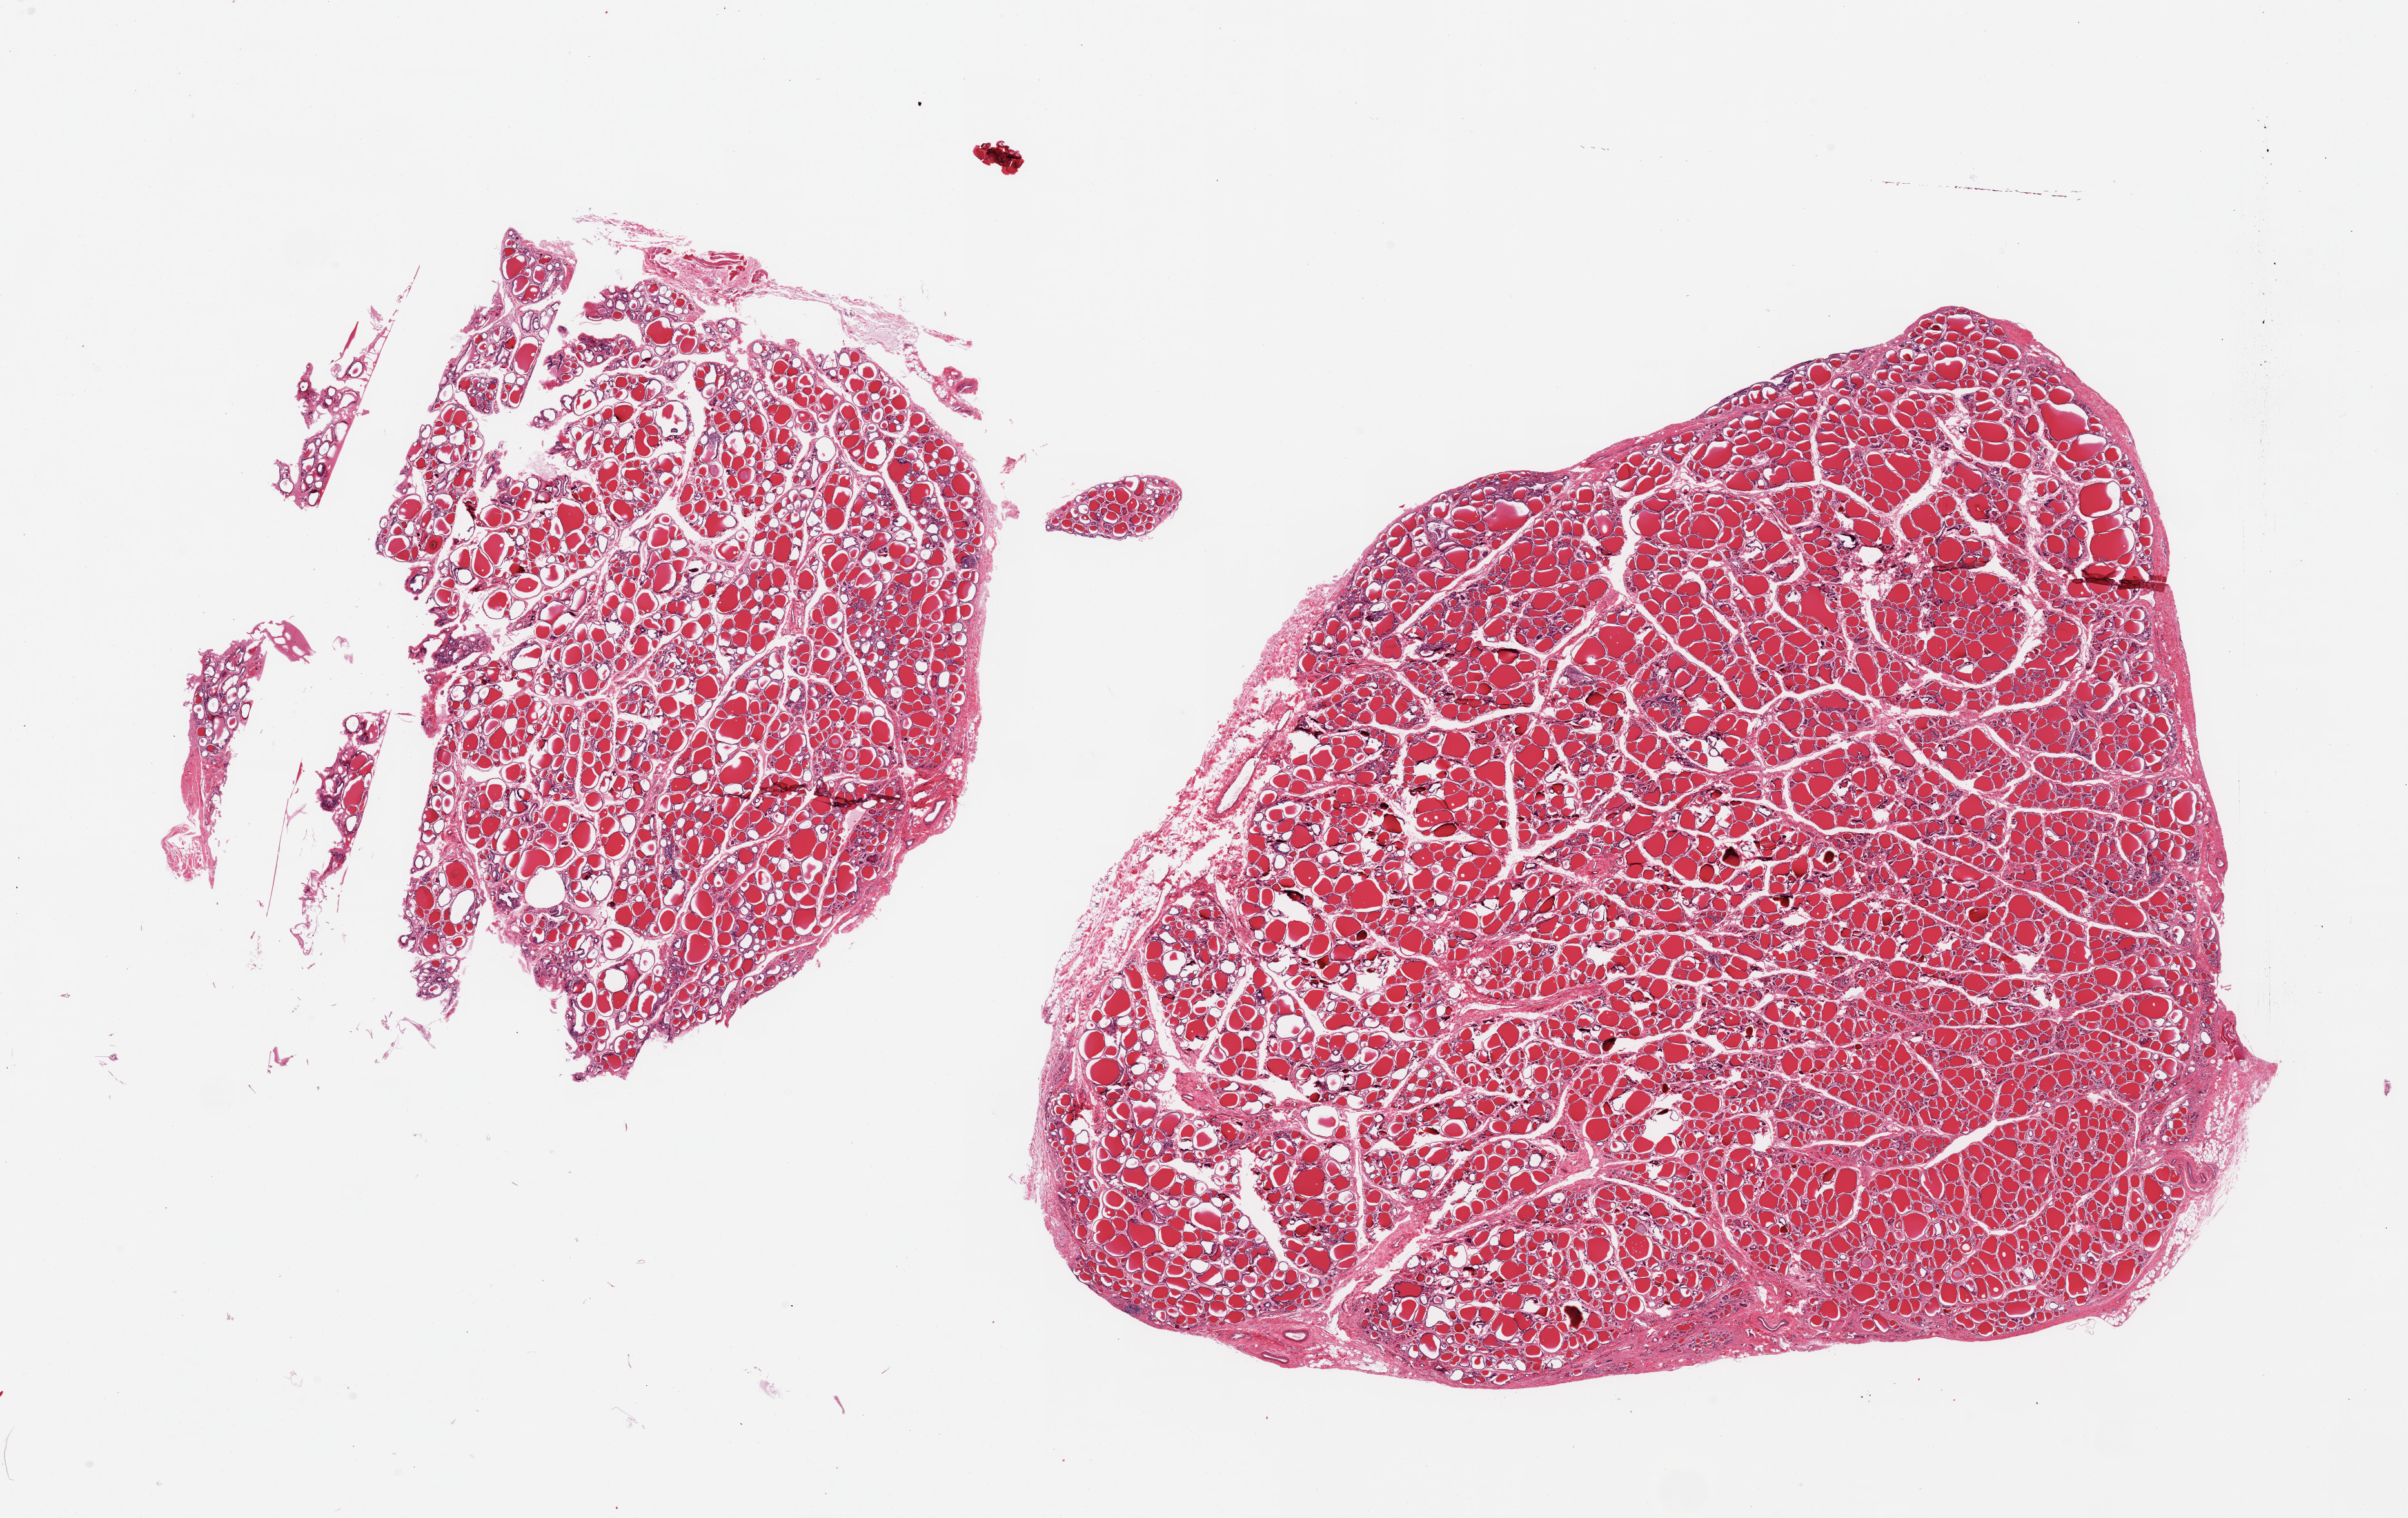
Hematoxylin and eosin (H&E) whole-slide image — whole scanned area (about 29.5 x 18.6 mm, acquisition: 20x scan) shown as a low-resolution overview. PAXgene-fixed, paraffin-embedded tissue. Section of thyroid (target tissue). Tissue donor sample.
Pathologist's review note for this sample: 2 pieces; trace of external fat.